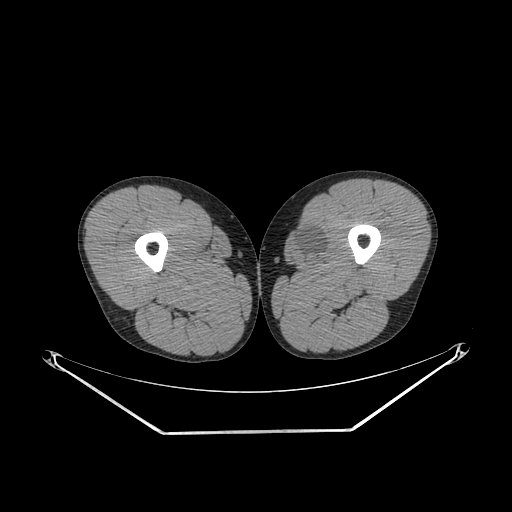
CT of an extremity soft-tissue mass (from a PET/CT study), one axial slice; position 260 of 311 along the scan axis; reconstruction kernel SOFT; 140 kVp; soft-tissue window (W 400 / L 40 HU); 3.75 mm slice thickness; 512 × 512 image matrix, field of view 500 × 500 mm. Male patient. From the clinical record (not read from this slice): histological type: mixoid liposarcoma; grade: low; site of the primary tumour: left thigh.
Annotated regions visible in this slice (expert contour drawn on MRI and transferred to this co-registered scan by the dataset authors):
- gross tumour volume (mass): box from (x=297, y=230) to (x=325, y=257) px